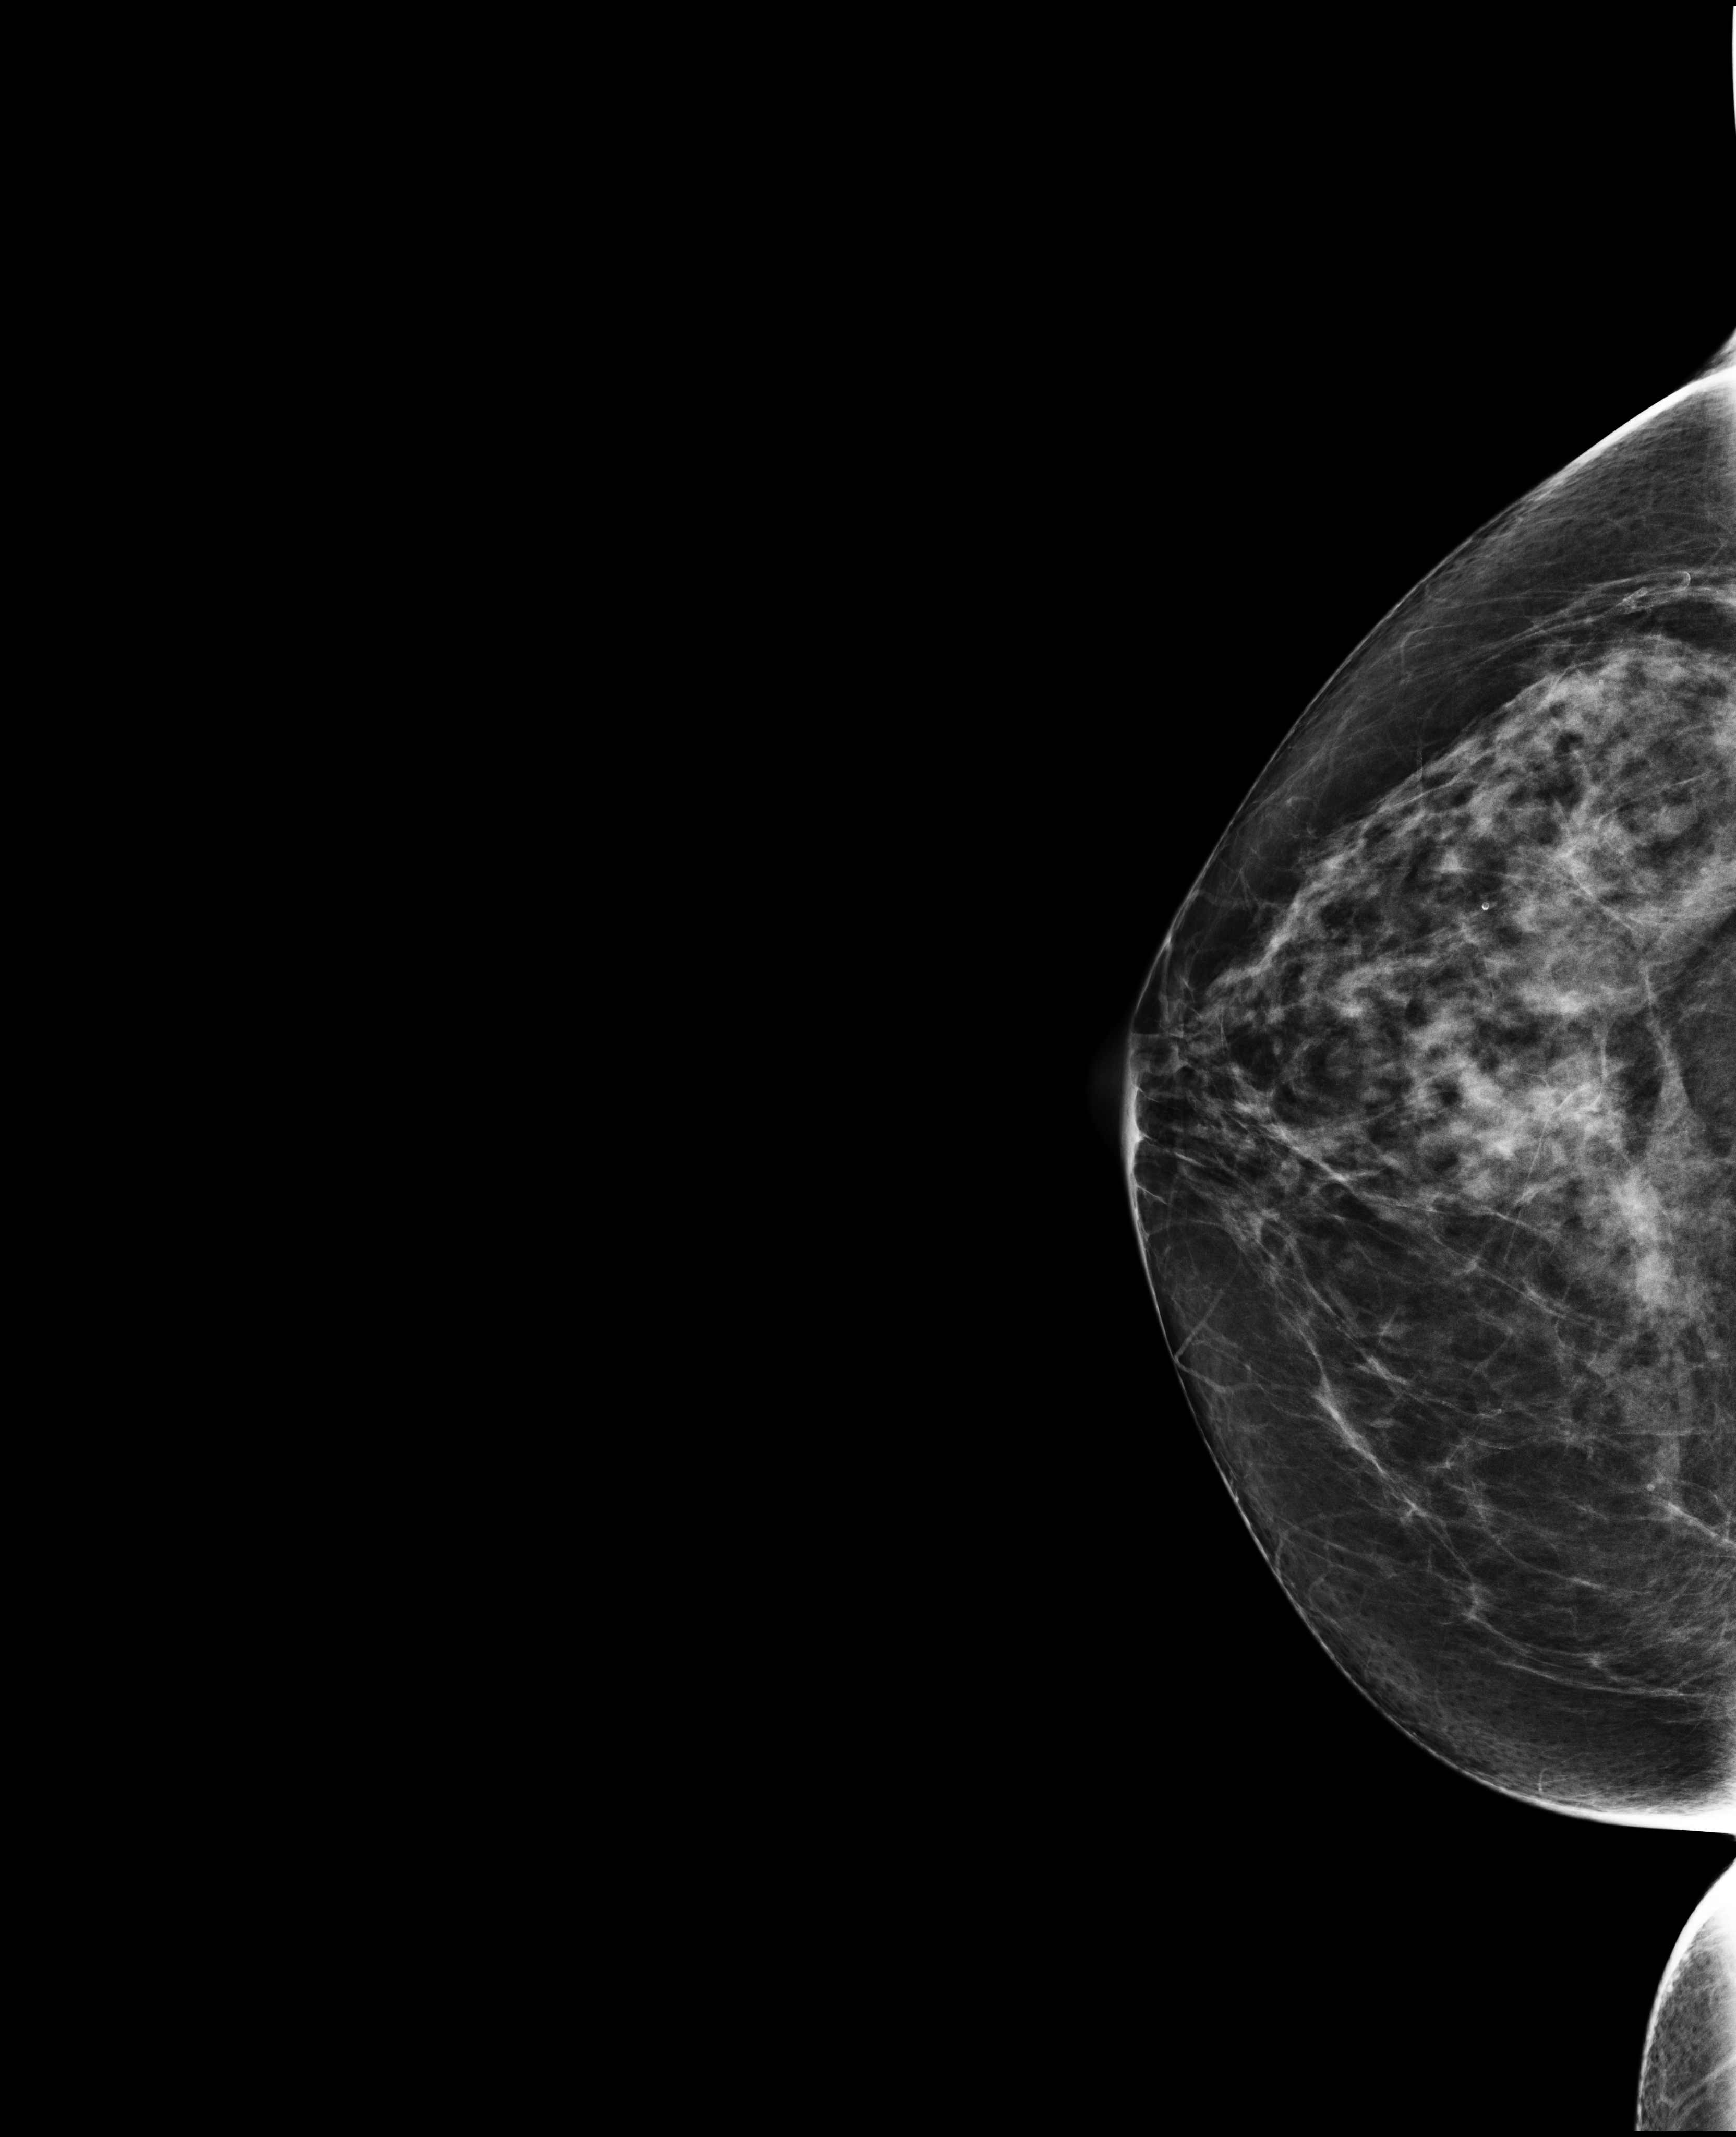
Screening examination. Patient: female, 68 years.
Image type: full-field digital mammogram. Breast: right. Projection: craniocaudal (CC) view.